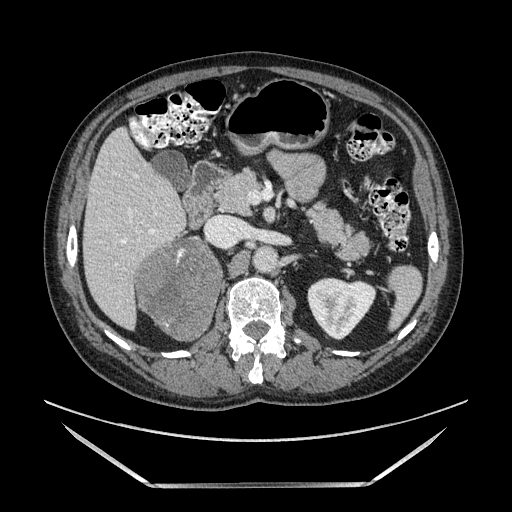
Contrast-enhanced abdominal CT, one axial slice. Slice 71 of 185 in the series (ordered by position). Soft-tissue window (W 400 / L 40 HU). 1.25 mm slice thickness. 512 × 512 image matrix, field of view 440 × 440 mm. Male patient. From the clinical record (not read from this slice): diagnosis: adrenocortical carcinoma; tumour side: right adrenal; tumour size at pathology: 10.3 cm; Ki-67 index: 20 %; stage (as recorded): 3.
Structures marked on this image (semi-automatically segmented with operator editing):
- mass: bounding box [x1, y1, x2, y2] px = [138, 239, 219, 341]